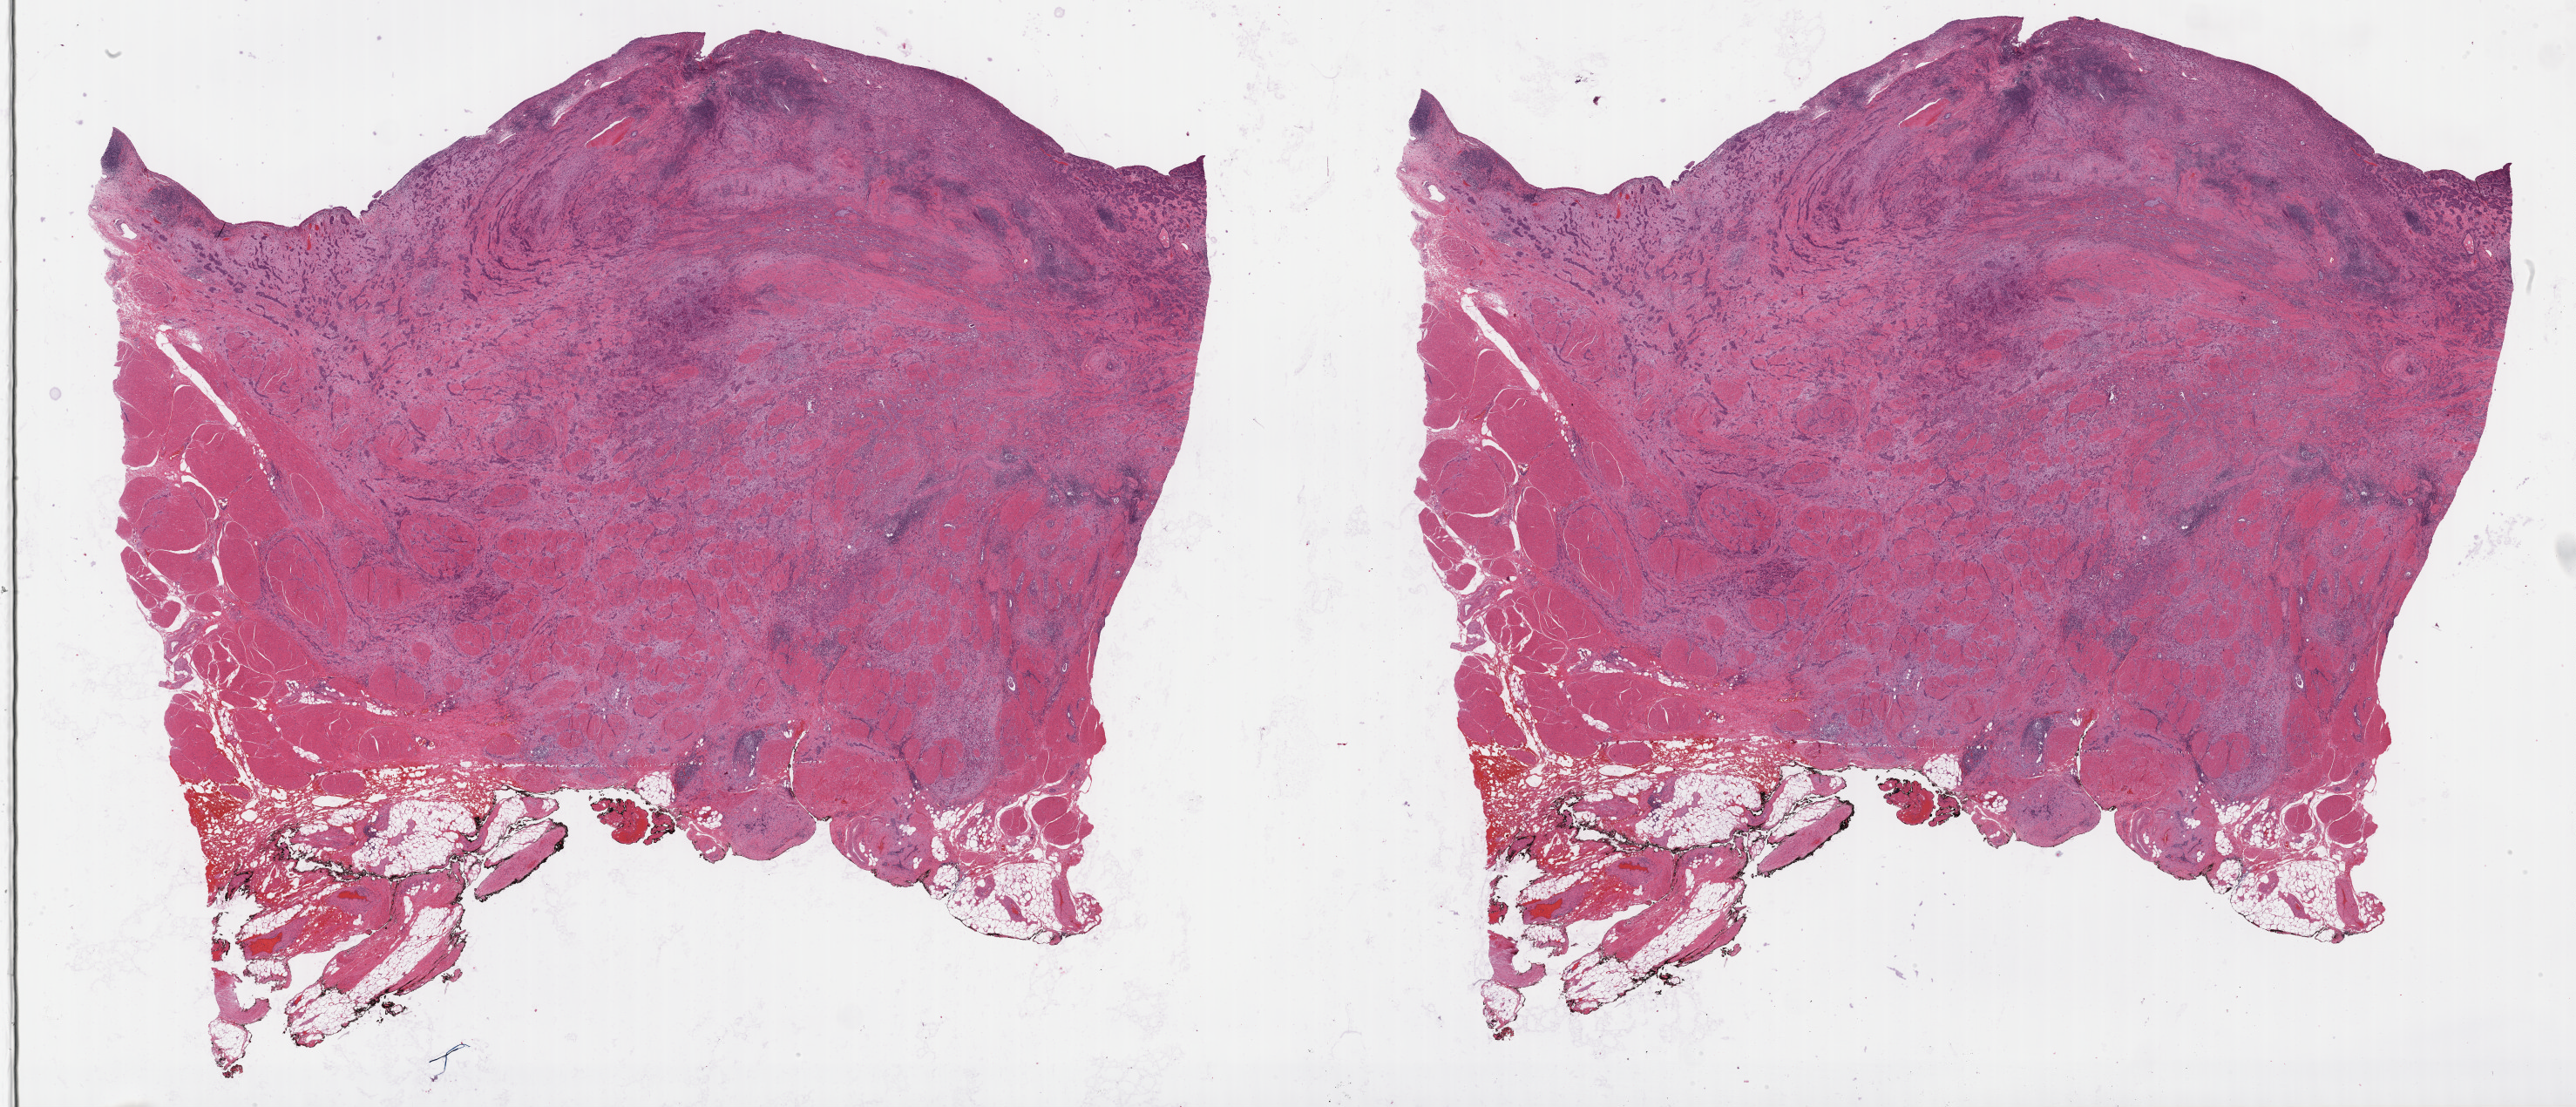
Whole-slide histology image, Hematoxylin and eosin (H&E) stained — low-resolution overview of the scanned area, about 47.8 x 20.5 mm, formalin-fixed paraffin-embedded (FFPE) diagnostic section, primary tumour sample from the bladder. Patient: female, age at initial diagnosis 60 years. Histologic grade: high grade.
- AJCC pathologic stage: III (7th edition)
- lymph nodes positive (case pathology): 0 of 24 examined
- histologic diagnosis: Transitional cell carcinoma (posterior wall of bladder)